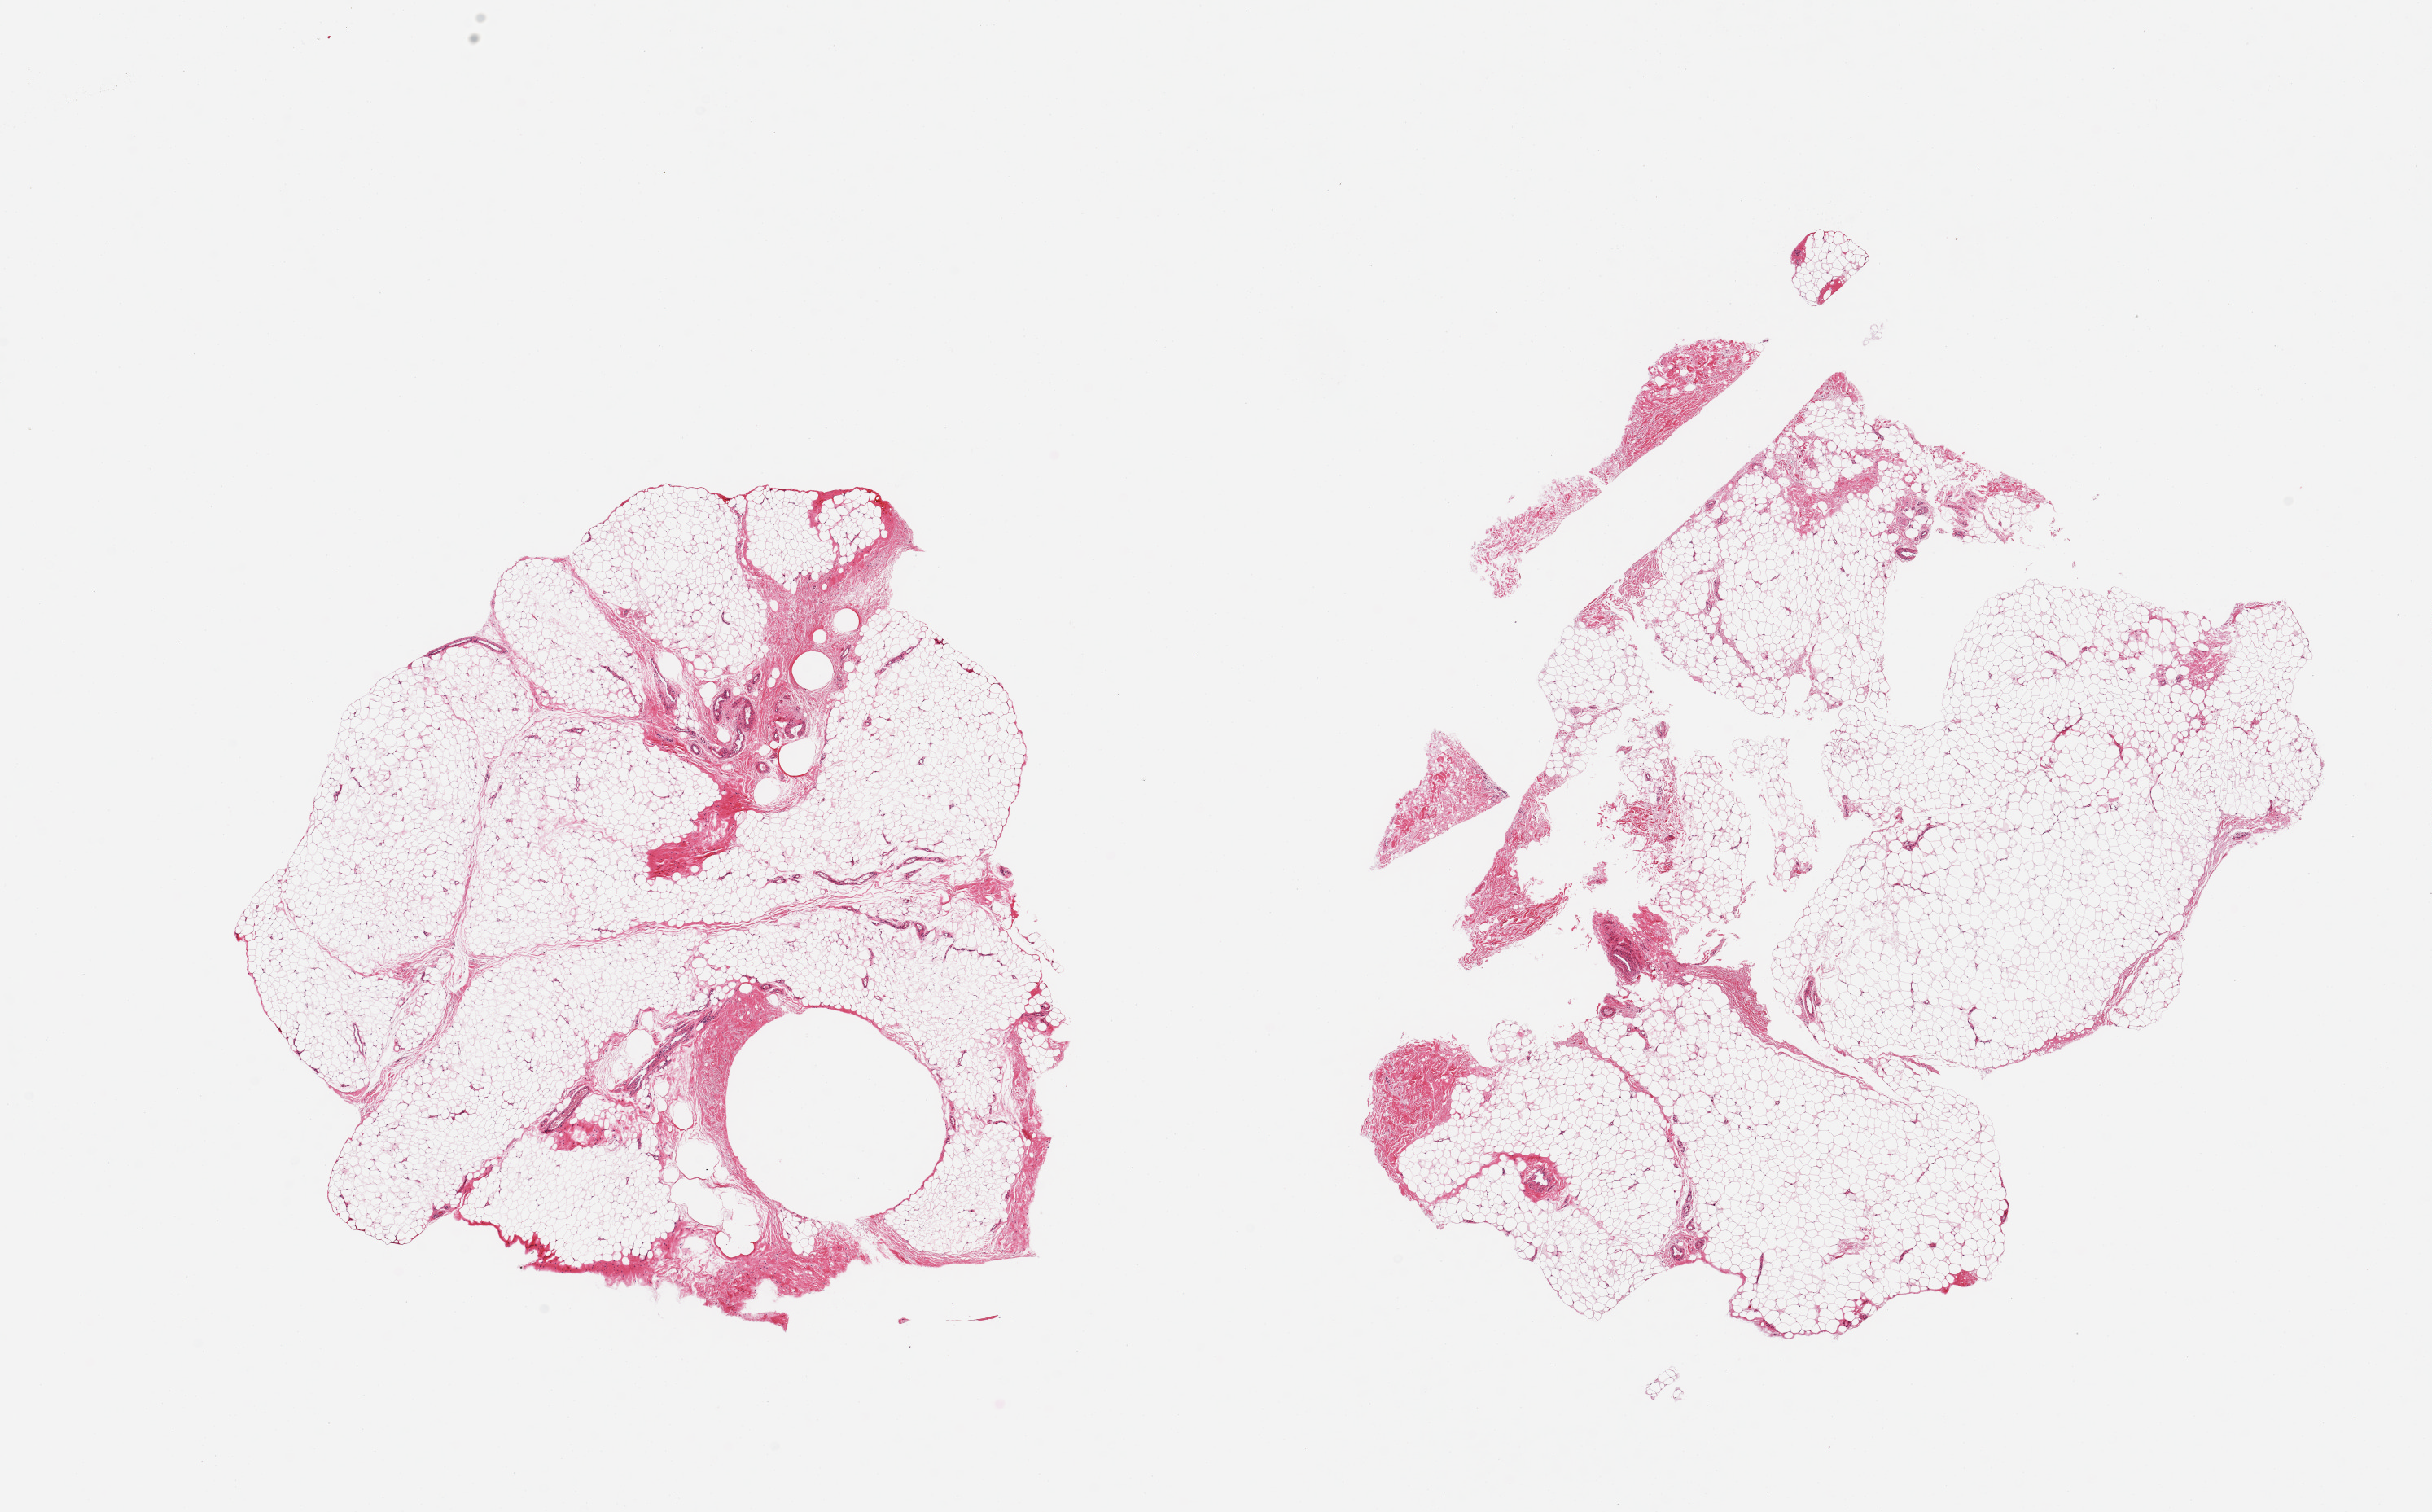
Haematoxylin and eosin whole-slide image, whole scanned area (about 23.6 x 14.7 mm) shown as a low-resolution overview. PAXgene-fixed paraffin-embedded (PFPE) section. Section of adipose tissue (target tissue). Donor tissue sample. Male donor.
Pathologist's review note for this sample: 2 pieces, 10-15% fascia/vascular elements.